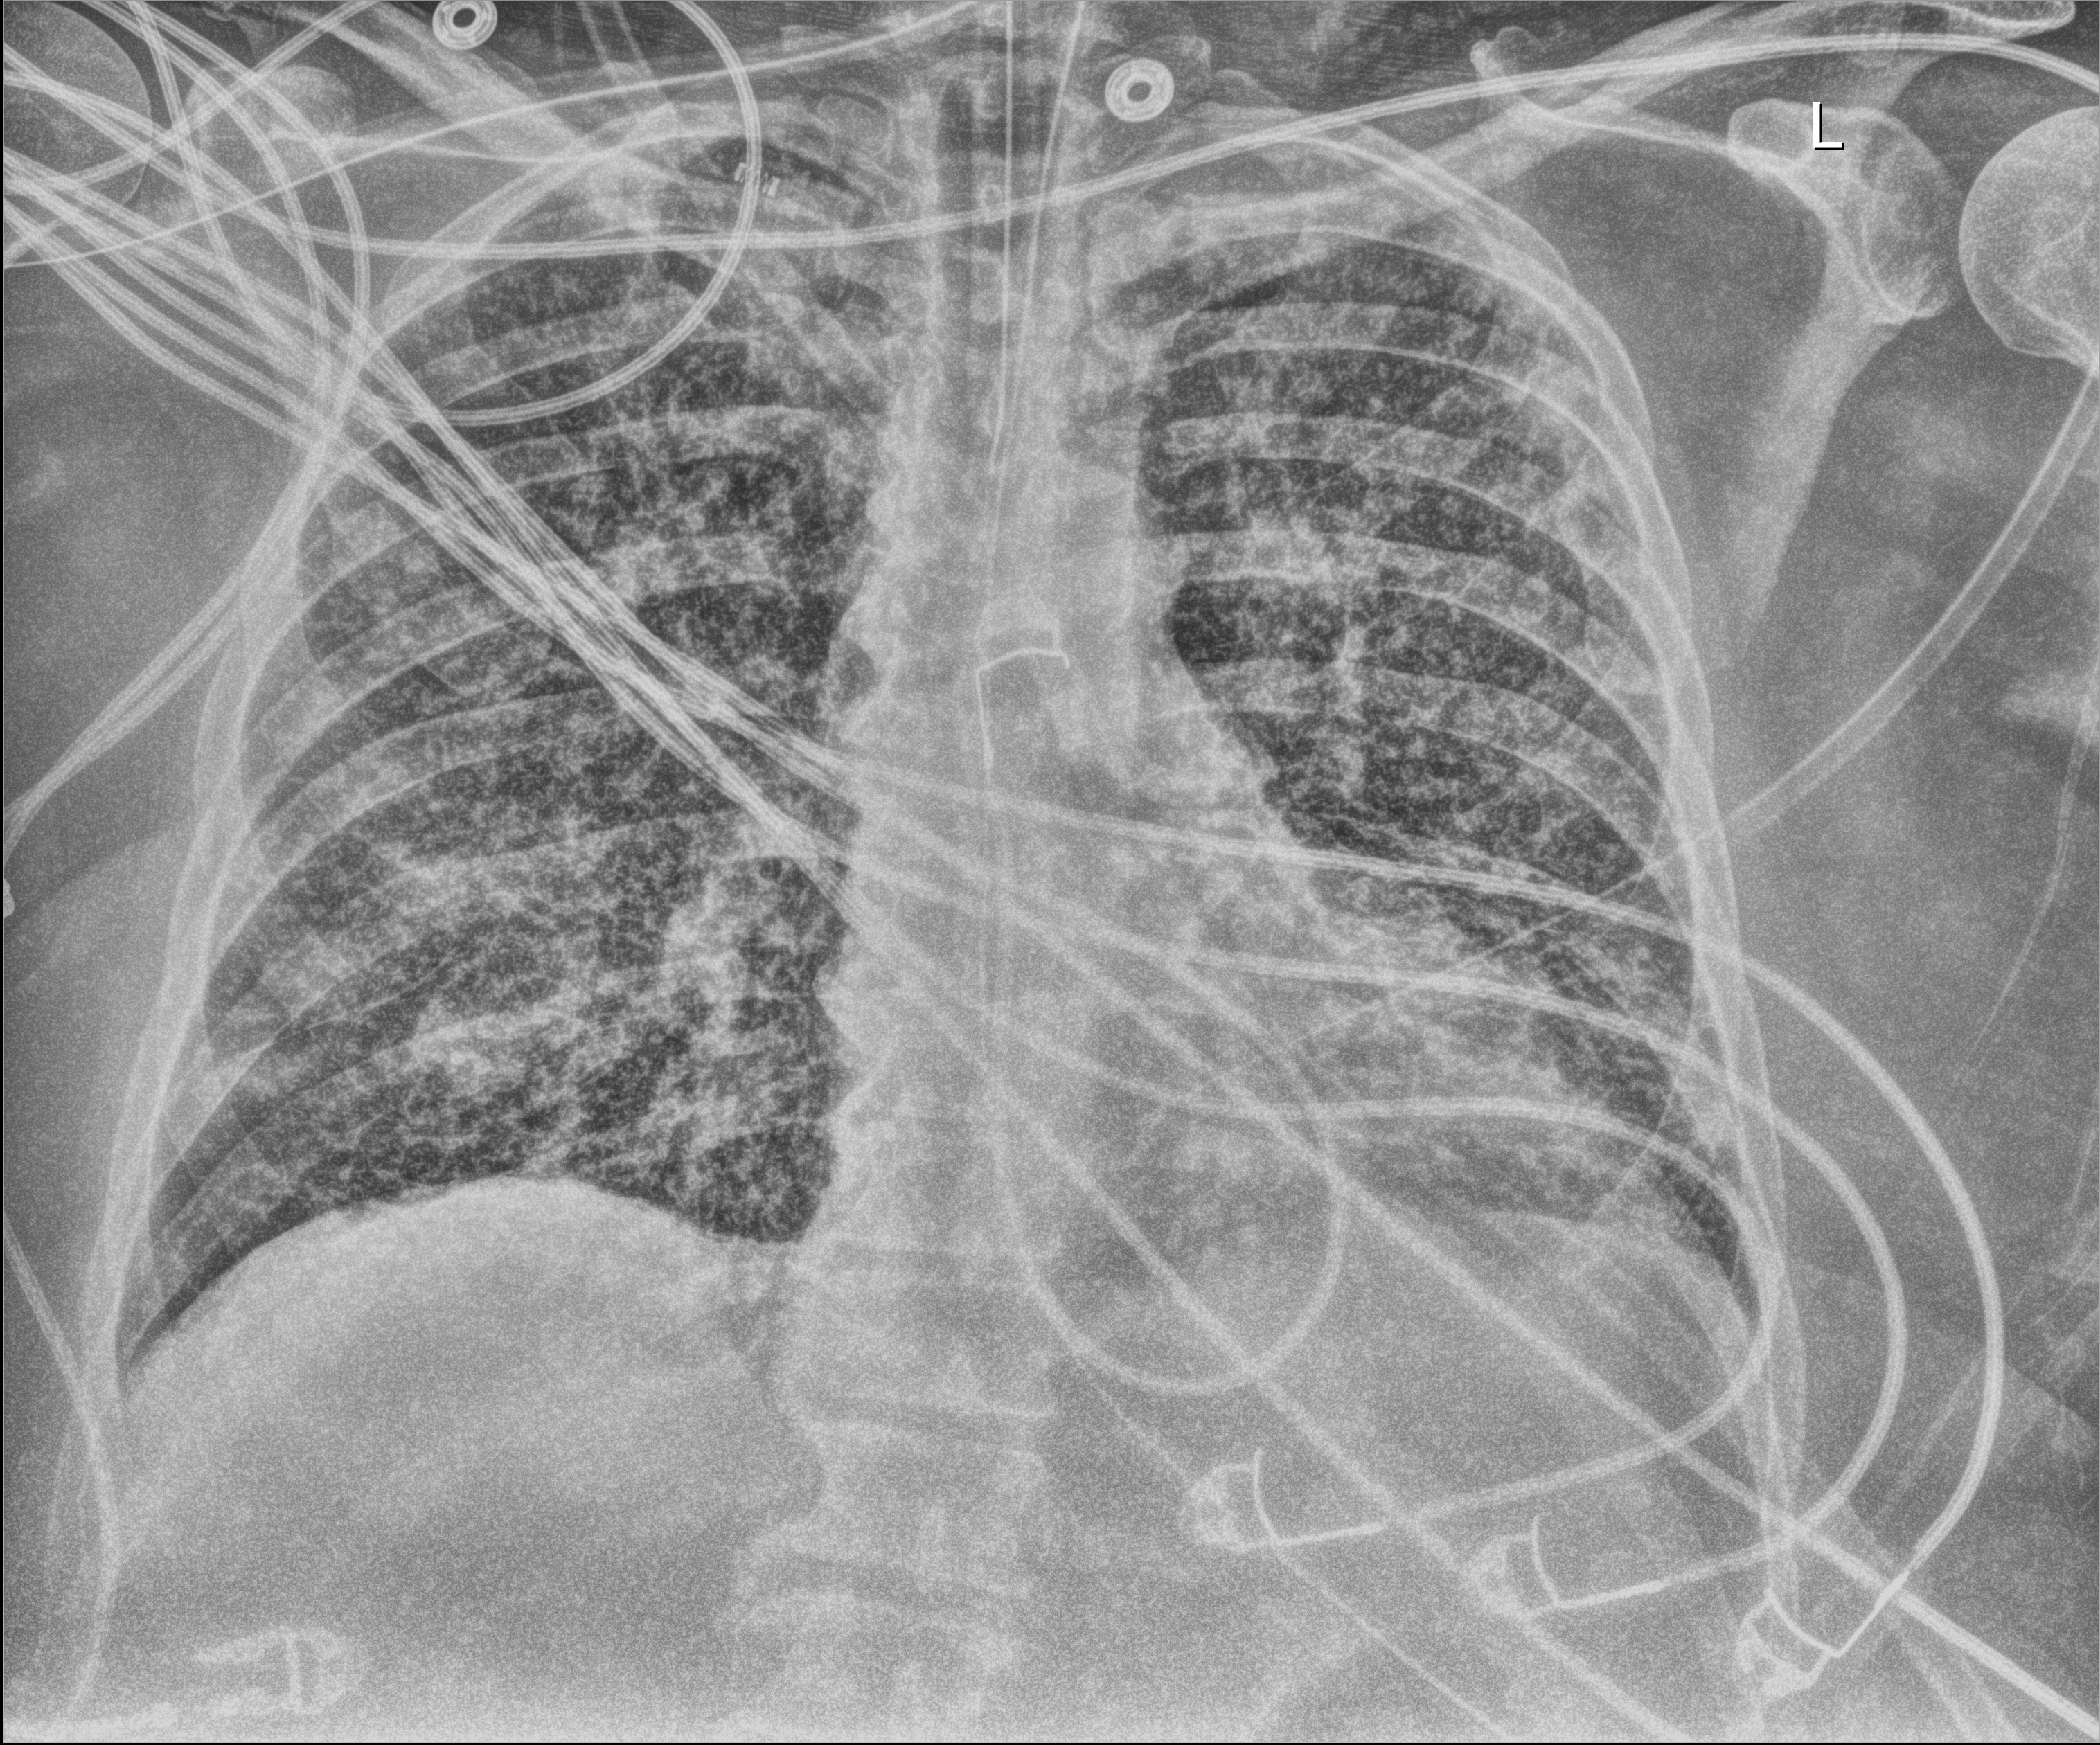
Chest radiograph, anteroposterior (AP) projection. Patient hospitalised with COVID-19, aged 18–59 years.
Admission-level facts for this patient (not findings on this image; timing relative to this image not recorded): admitted to intensive care during this hospital stay: yes.